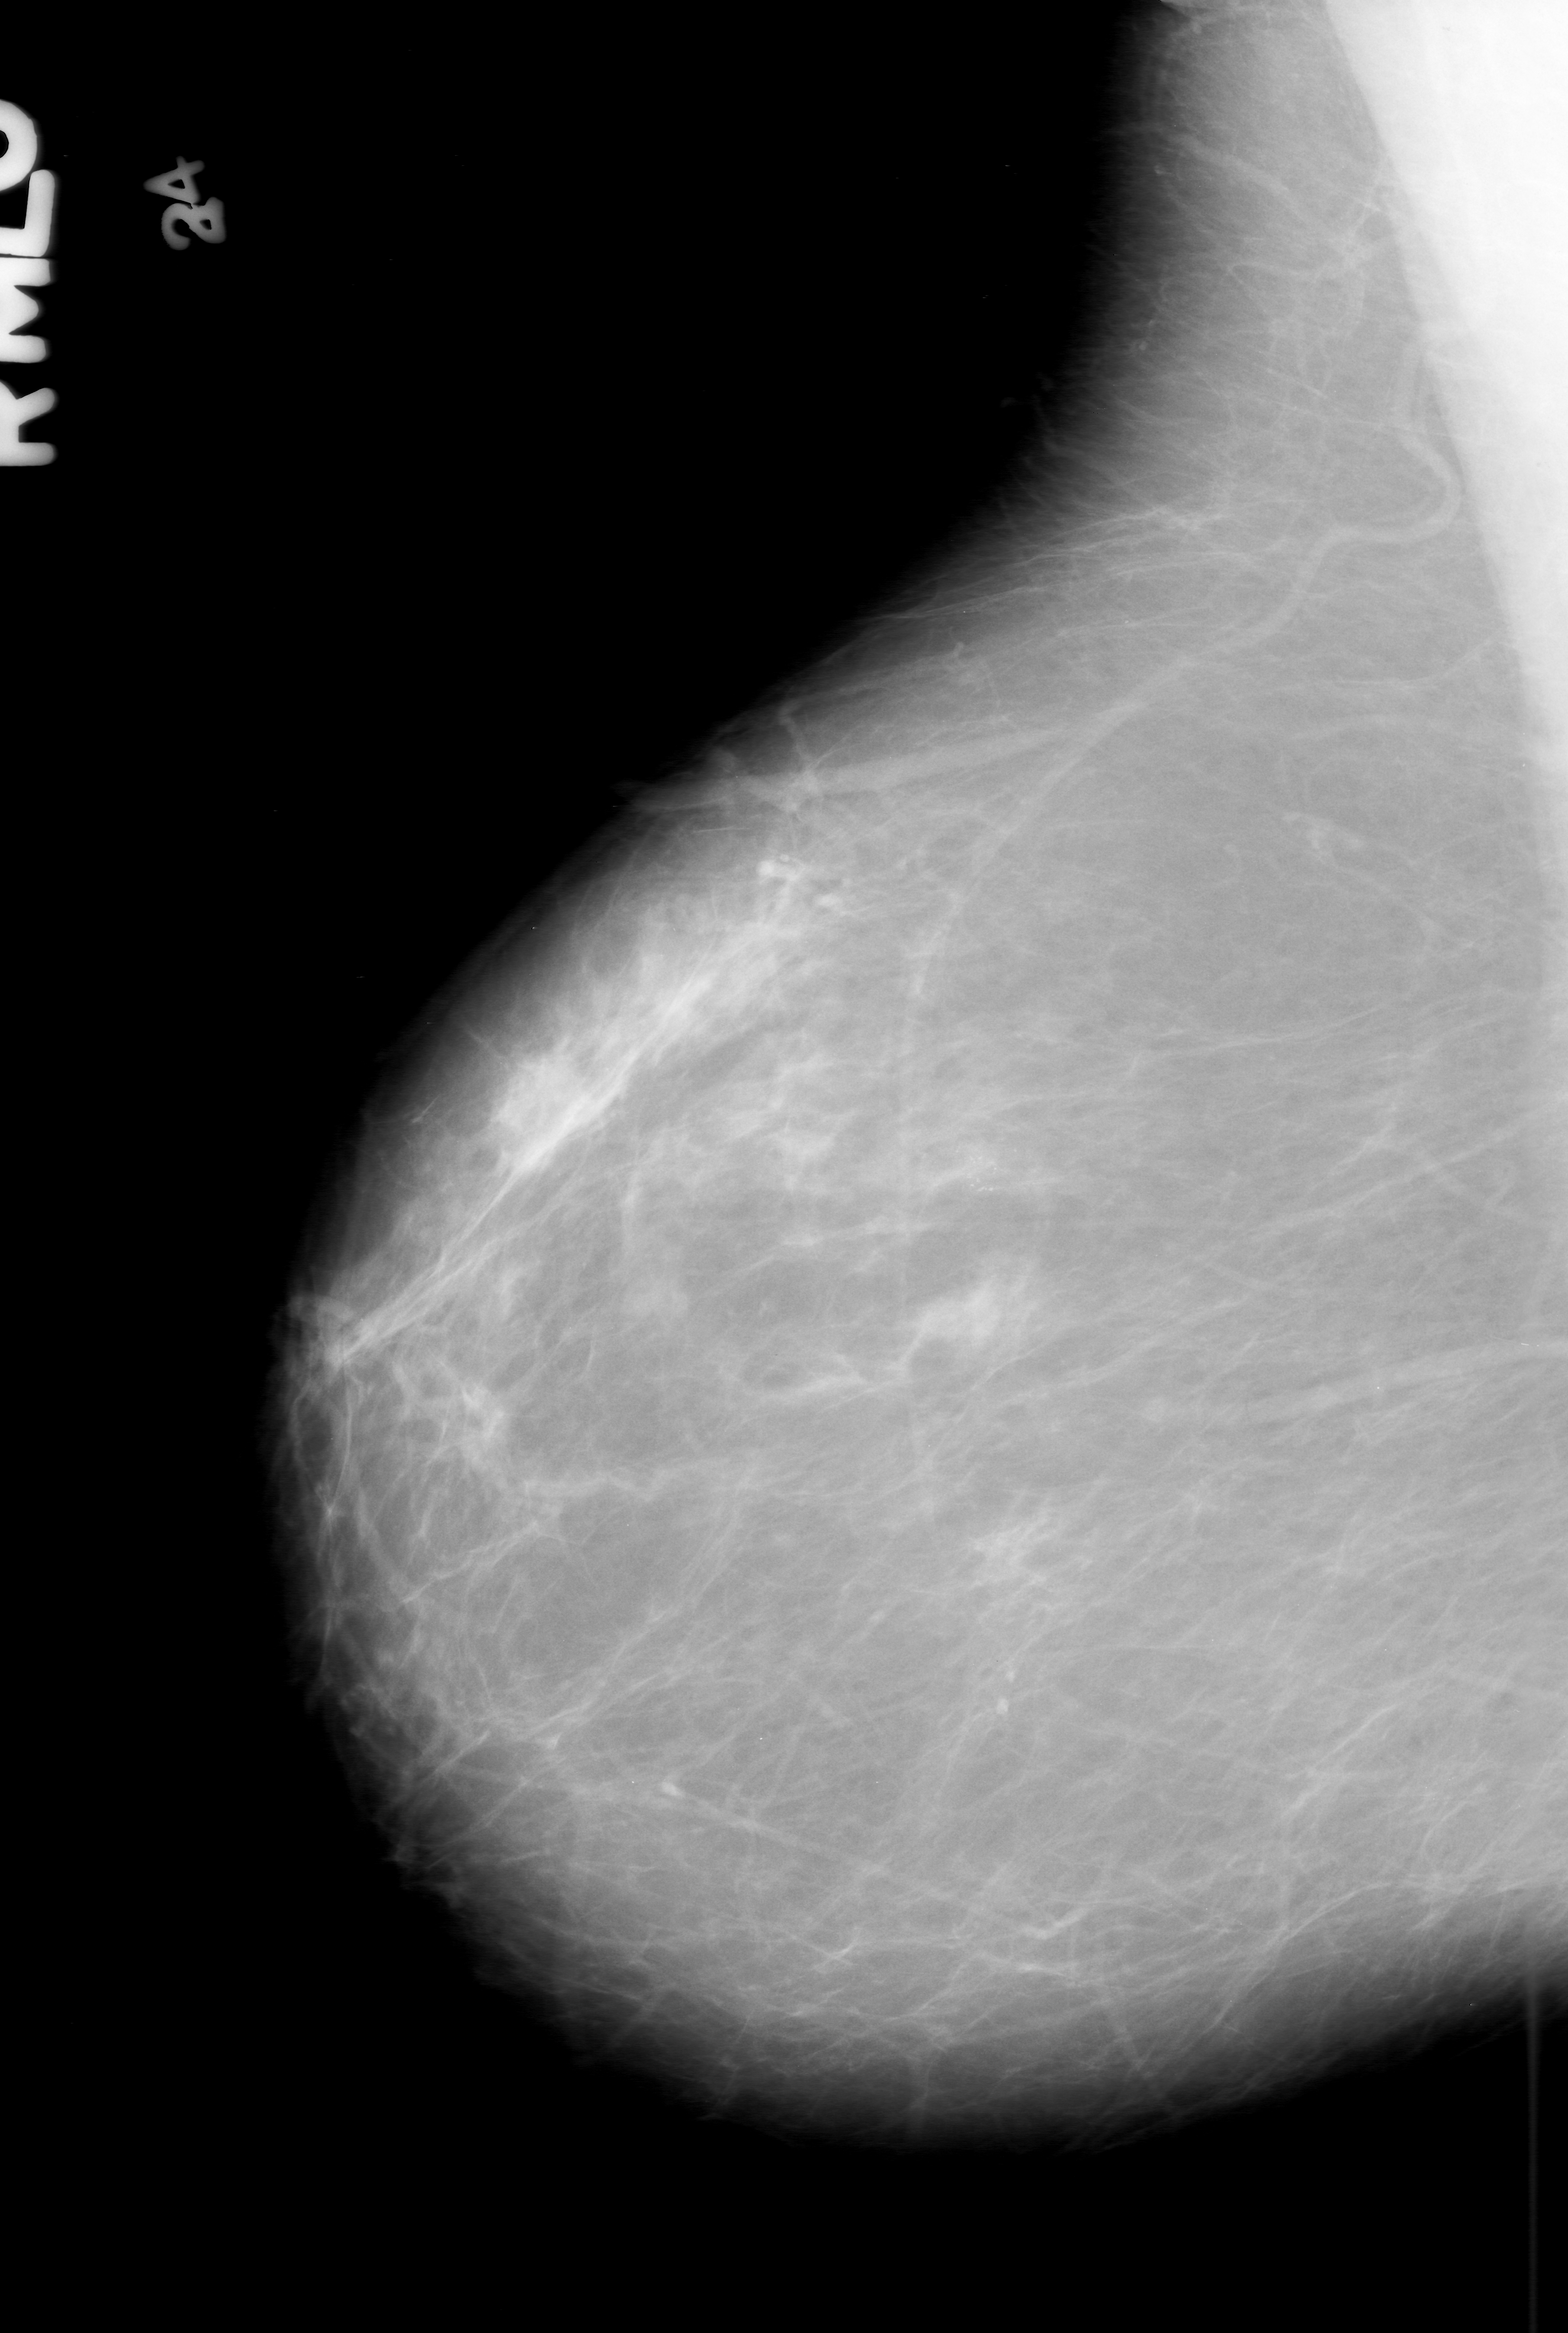
Scanned film-screen mammogram; right breast; mediolateral oblique (MLO) view; BI-RADS breast density category 2 (scale 1–4); 1568 × 2333 image matrix.
Expert-marked regions of interest on this image (one box per marked abnormality):
- calcifications, morphology pleomorphic, distribution clustered; BI-RADS assessment category 0 (incomplete: needs additional imaging); pathology (as recorded): benign: bounding box <874,1078,1091,1251> (left, top, right, bottom; pixels)